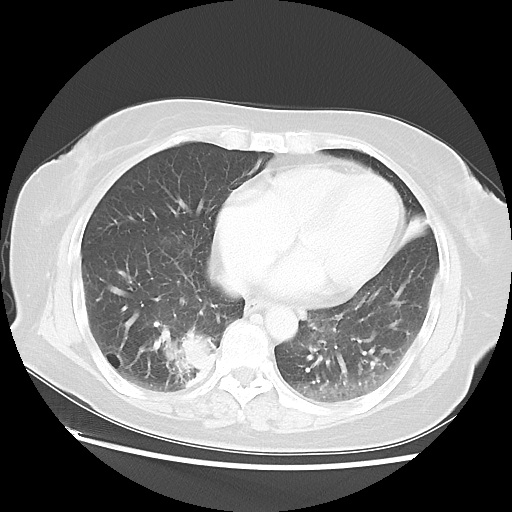
Chest CT, one axial slice. Position 21 of 52 along the scan axis. Lung window (W 1500 / L -600 HU). 5 mm slice thickness. 512 × 512 image matrix. Female patient, age 69 years. From the clinical record (not read from this slice): clinical TNM (as recorded): T2 N1 M1a.
Structures marked on this image (bounding box drawn by a radiologist):
- lung tumour (recorded histology: adenocarcinoma): bounding box <171,328,217,392> (left, top, right, bottom; pixels)